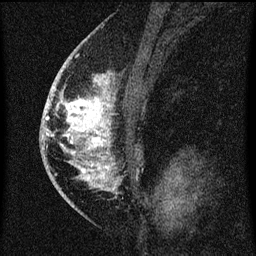
Breast MRI (dynamic contrast-enhanced), one sagittal slice; position 40 of 60 along the scan axis; dynamic contrast-enhanced series, image 2 of 3 at this slice position (ordered by acquisition); 1.5 T; TE 4.2 ms, TR 8 ms; 2 mm slice thickness; 256 × 256 image matrix, field of view 180 × 180 mm. Patient: female, 46 years.
Outlined on this slice (semi-automatically segmented with operator editing):
- analysis volume of interest (the breast-tissue region the enhancement analysis was run in; not a lesion): box from (x=52, y=68) to (x=117, y=195) px
- tumour enhancement mask (voxels above the 70 % enhancement threshold inside the analysis volume of interest): (x=52, y=68)–(x=116, y=191)